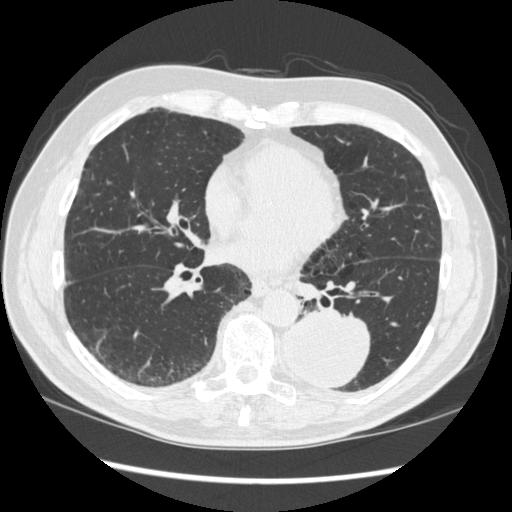
Low-dose screening chest CT, axial slice, baseline annual screen, lung window (W 1500 / L -600 HU), 512 × 512 image matrix, field of view 360 × 360 mm. Male, age 72 years at enrolment. Current smoker at enrolment.
Expert reader's lesion annotation, box from (x=269, y=301) to (x=373, y=392) px. The screening reader recorded 2 non-calcified nodules or masses ≥4 mm on this exam (left lower lobe, right middle lobe); which of them this box marks is not recorded. Participant outcome: lung cancer diagnosed 37 days after this screen — squamous cell carcinoma, NOS, left lower lobe, stage IIIA (AJCC 6th edition), 60 mm at pathology.